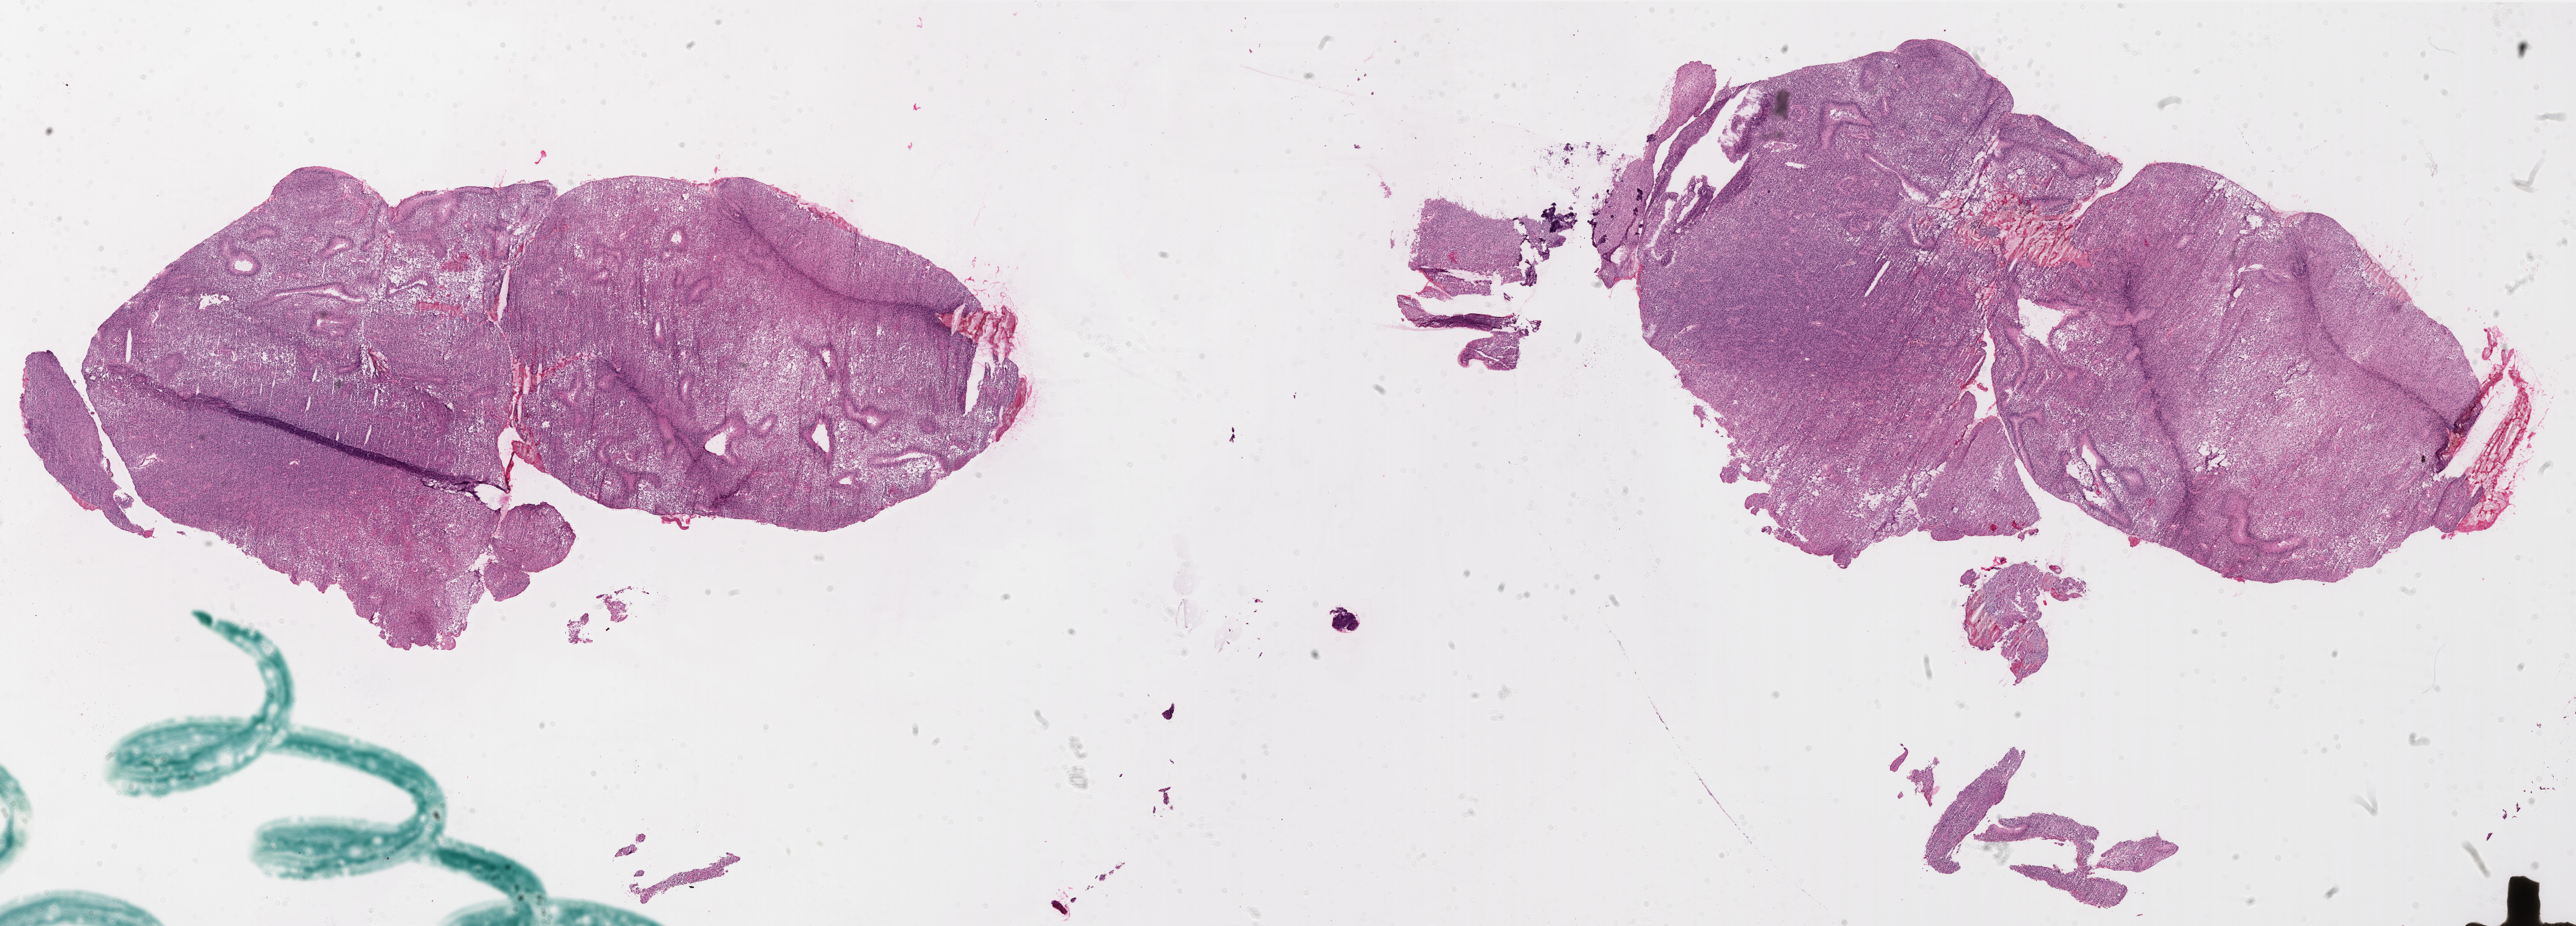
Digitized H&E-stained tissue section (whole slide), a low-resolution overview of the entire scanned area, about 41.0 x 14.7 mm (acquisition: 20x scan). Frozen section. Sample: primary tumour, brain. Patient: female, age at initial diagnosis 37 years. Slide review estimates, as recorded: tumour cells 90%, tumour nuclei 100%, normal cells 0%, stromal cells 0%, necrosis 10%.
Diagnosis: Glioblastoma.